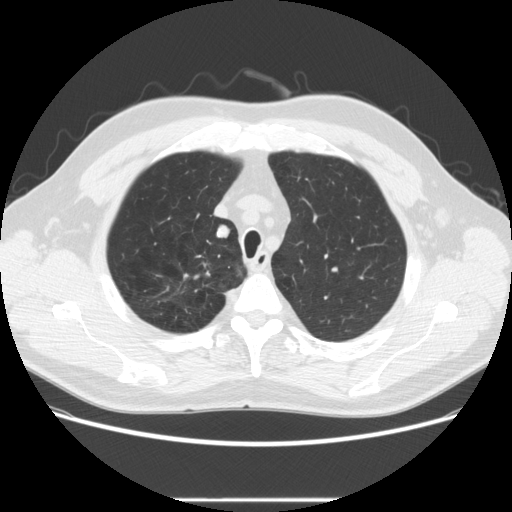
Axial slice from a low-dose chest CT screening exam. Baseline annual screen. Lung window (W 1500 / L -600 HU). 2.5 mm slice thickness. Slice 47 of 270 in the series. 512 × 512 image matrix, field of view 380 × 380 mm. Male participant, aged 64 years at enrolment.
Lesion marked by an expert reader, bounding box [x1, y1, x2, y2] px = [198, 220, 238, 251]. The screening reader recorded 2 non-calcified nodules or masses ≥4 mm on this exam (right upper lobe, right upper lobe); which of them this box marks is not recorded. Official screen result: positive, change unspecified: nodule(s) >= 4 mm or enlarging nodule(s), mass(es), or other non-specific abnormalities suspicious for lung cancer. Later outcome: lung cancer diagnosed 753 days after this screen — adenocarcinoma, NOS, right upper lobe, moderately differentiated (G2), stage IA (AJCC 6th edition), 14 mm at pathology.